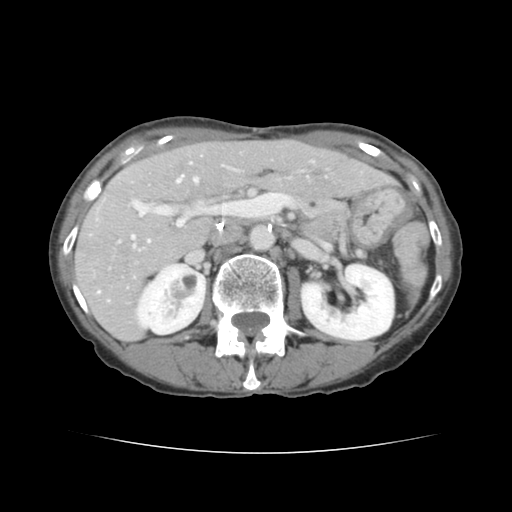
Contrast-enhanced abdominal CT, one axial slice. Slice 73 of 136 in the series (ordered by position). Intravenous contrast given. Soft-tissue window (W 400 / L 40 HU). 512 × 512 image matrix, field of view 319 × 319 mm. Female patient, age 77 years. Case-level facts recorded for this patient, not image findings: diagnosis: colorectal cancer liver metastases, imaged before liver resection; multiple liver metastases: yes; largest metastasis: 3 cm; disease in both lobes: no.
Structures marked on this image (manually delineated by an expert):
- hepatic veins: bounding box <131,176,198,239> (left, top, right, bottom; pixels)
- liver: <75,141,389,339>
- planned liver remnant (the part of the liver to remain after resection): <157,142,390,200>
- portal vein (with intrahepatic branches): <98,201,238,293>